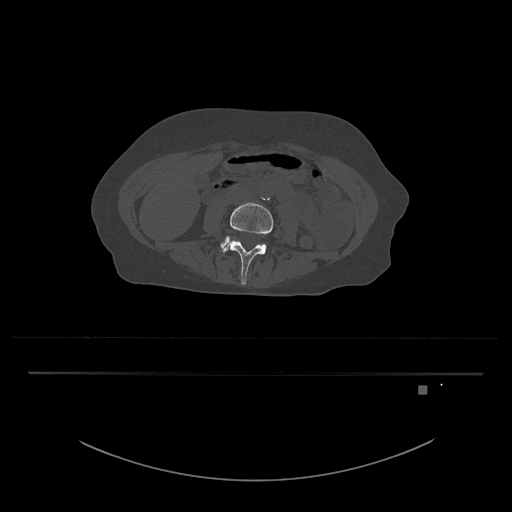
CT including the spine, one axial slice; position 357 of 797 along the scan axis; 120 kVp; bone window (W 1800 / L 400 HU); 512 × 512 image matrix. Female patient, age 57 years. From the clinical record (not read from this slice): primary cancer: cervical.
Outlined on this slice (semi-automatic segmentation, software-assisted and operator-edited):
- L4 vertebra: bounding box <222,202,273,285> (left, top, right, bottom; pixels)